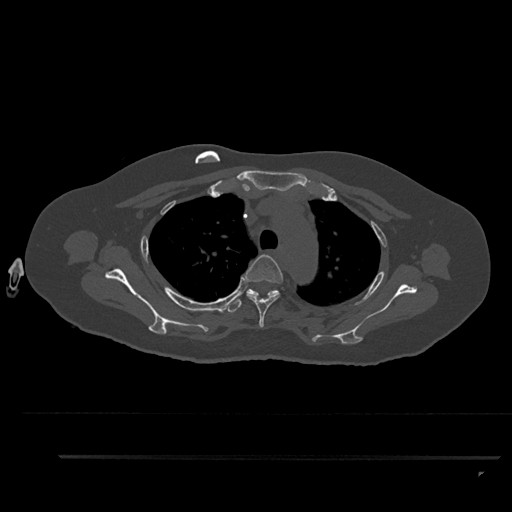
CT including the spine, one axial slice; bone window (W 1800 / L 400 HU); 0.5 mm slice thickness; 512 × 512 image matrix, field of view 408 × 408 mm. Patient: female, 44 years. From the clinical record (not read from this slice): primary cancer: renal.
Structures marked on this image (semi-automatically segmented with operator editing):
- T3 vertebra: bounding box (x1, y1, x2, y2) in pixels: (243, 254, 283, 328)
- T4 vertebra: (227, 289, 279, 313)